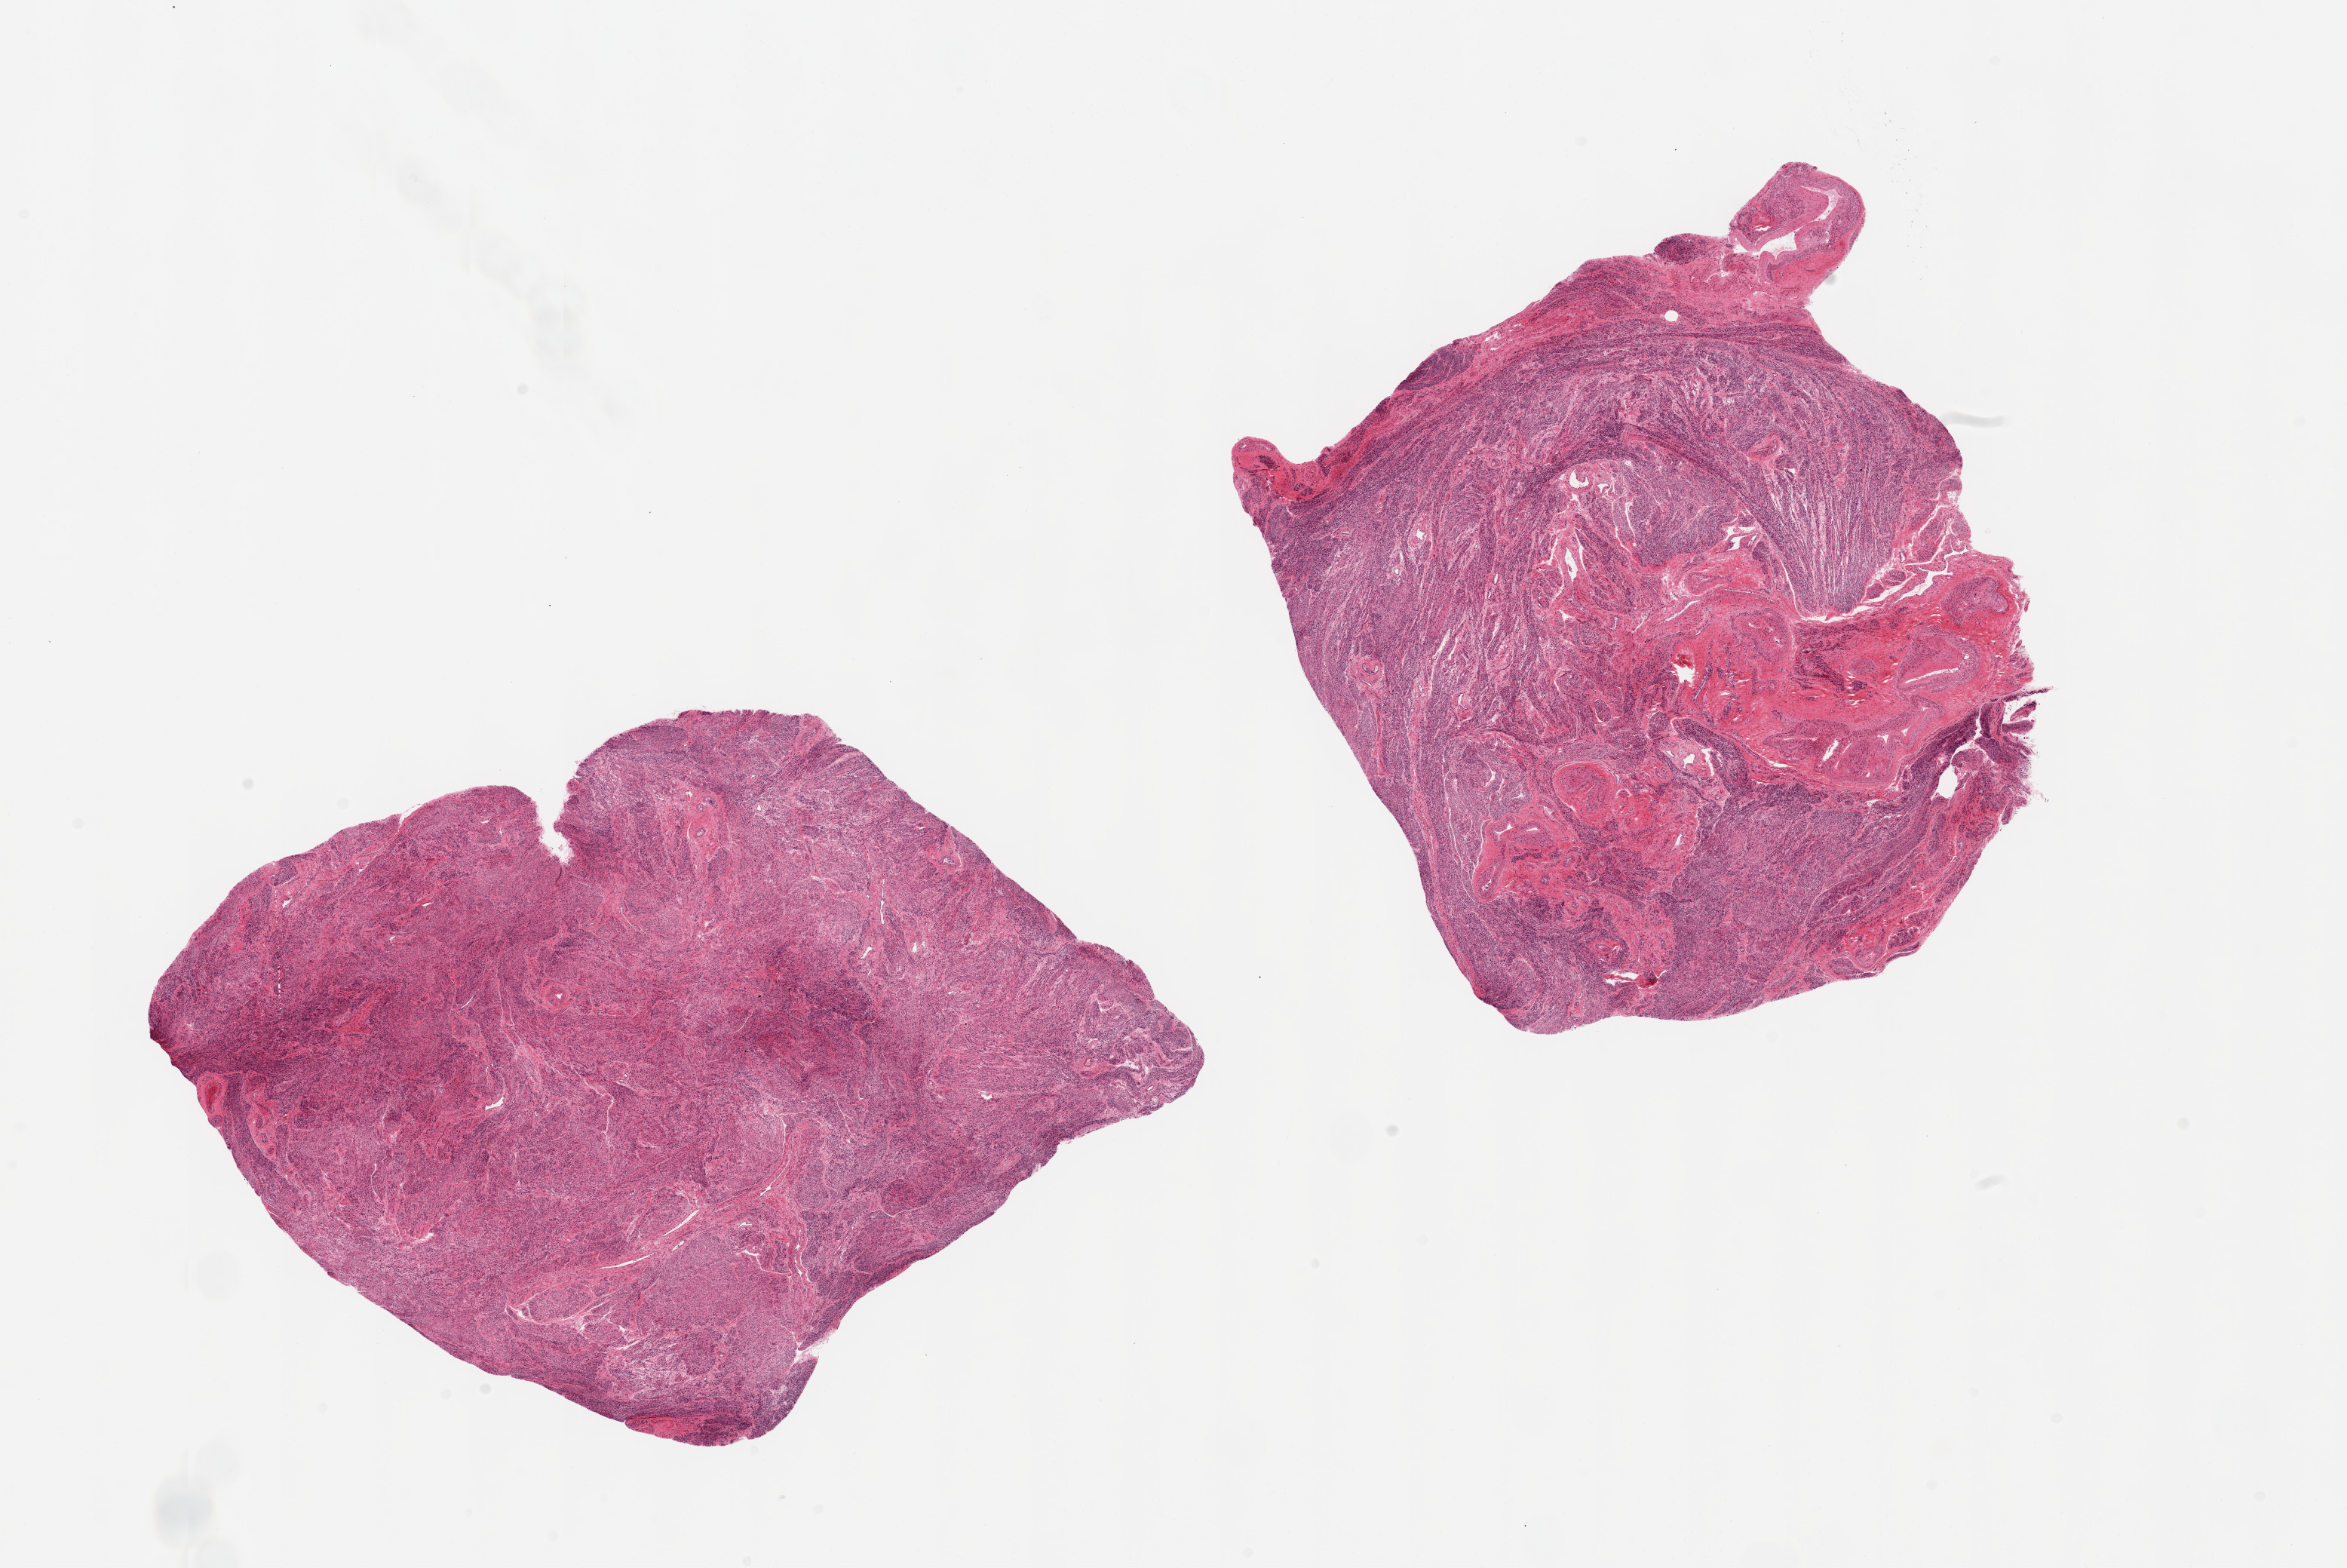
Haematoxylin and eosin whole-slide image — shown as a low-resolution overview of the whole scanned area (about 24.6 x 16.4 mm). PAXgene-fixed paraffin-embedded (PFPE) section. Target tissue: uterus. Donor tissue sample. Donor: female.
Reviewer comment on this tissue sample: 2 pieces; myometrium only in these cuts.